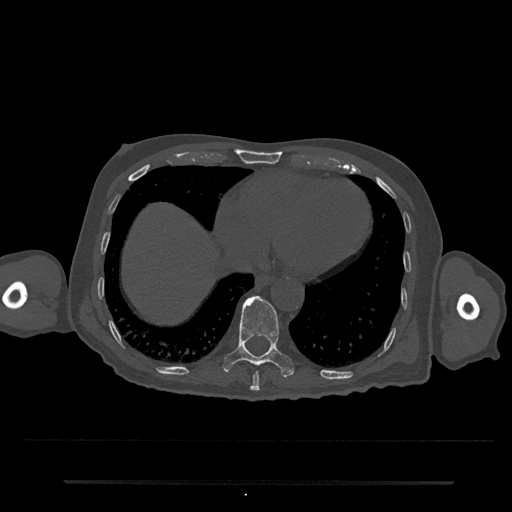
CT including the spine, one axial slice; position 319 of 797 along the scan axis; reconstruction kernel Br40s/3; 120 kVp; bone window (W 1800 / L 400 HU); 0.5 mm slice thickness; 512 × 512 image matrix, field of view 427 × 427 mm. Male patient, age 74 years. Case-level facts recorded for this patient, not image findings: primary cancer: prostate.
Annotated regions visible in this slice (semi-automatically segmented with operator editing):
- T10 vertebra: bounding box [x1, y1, x2, y2] px = [222, 296, 294, 378]
- T9 vertebra: [250, 372, 260, 392]